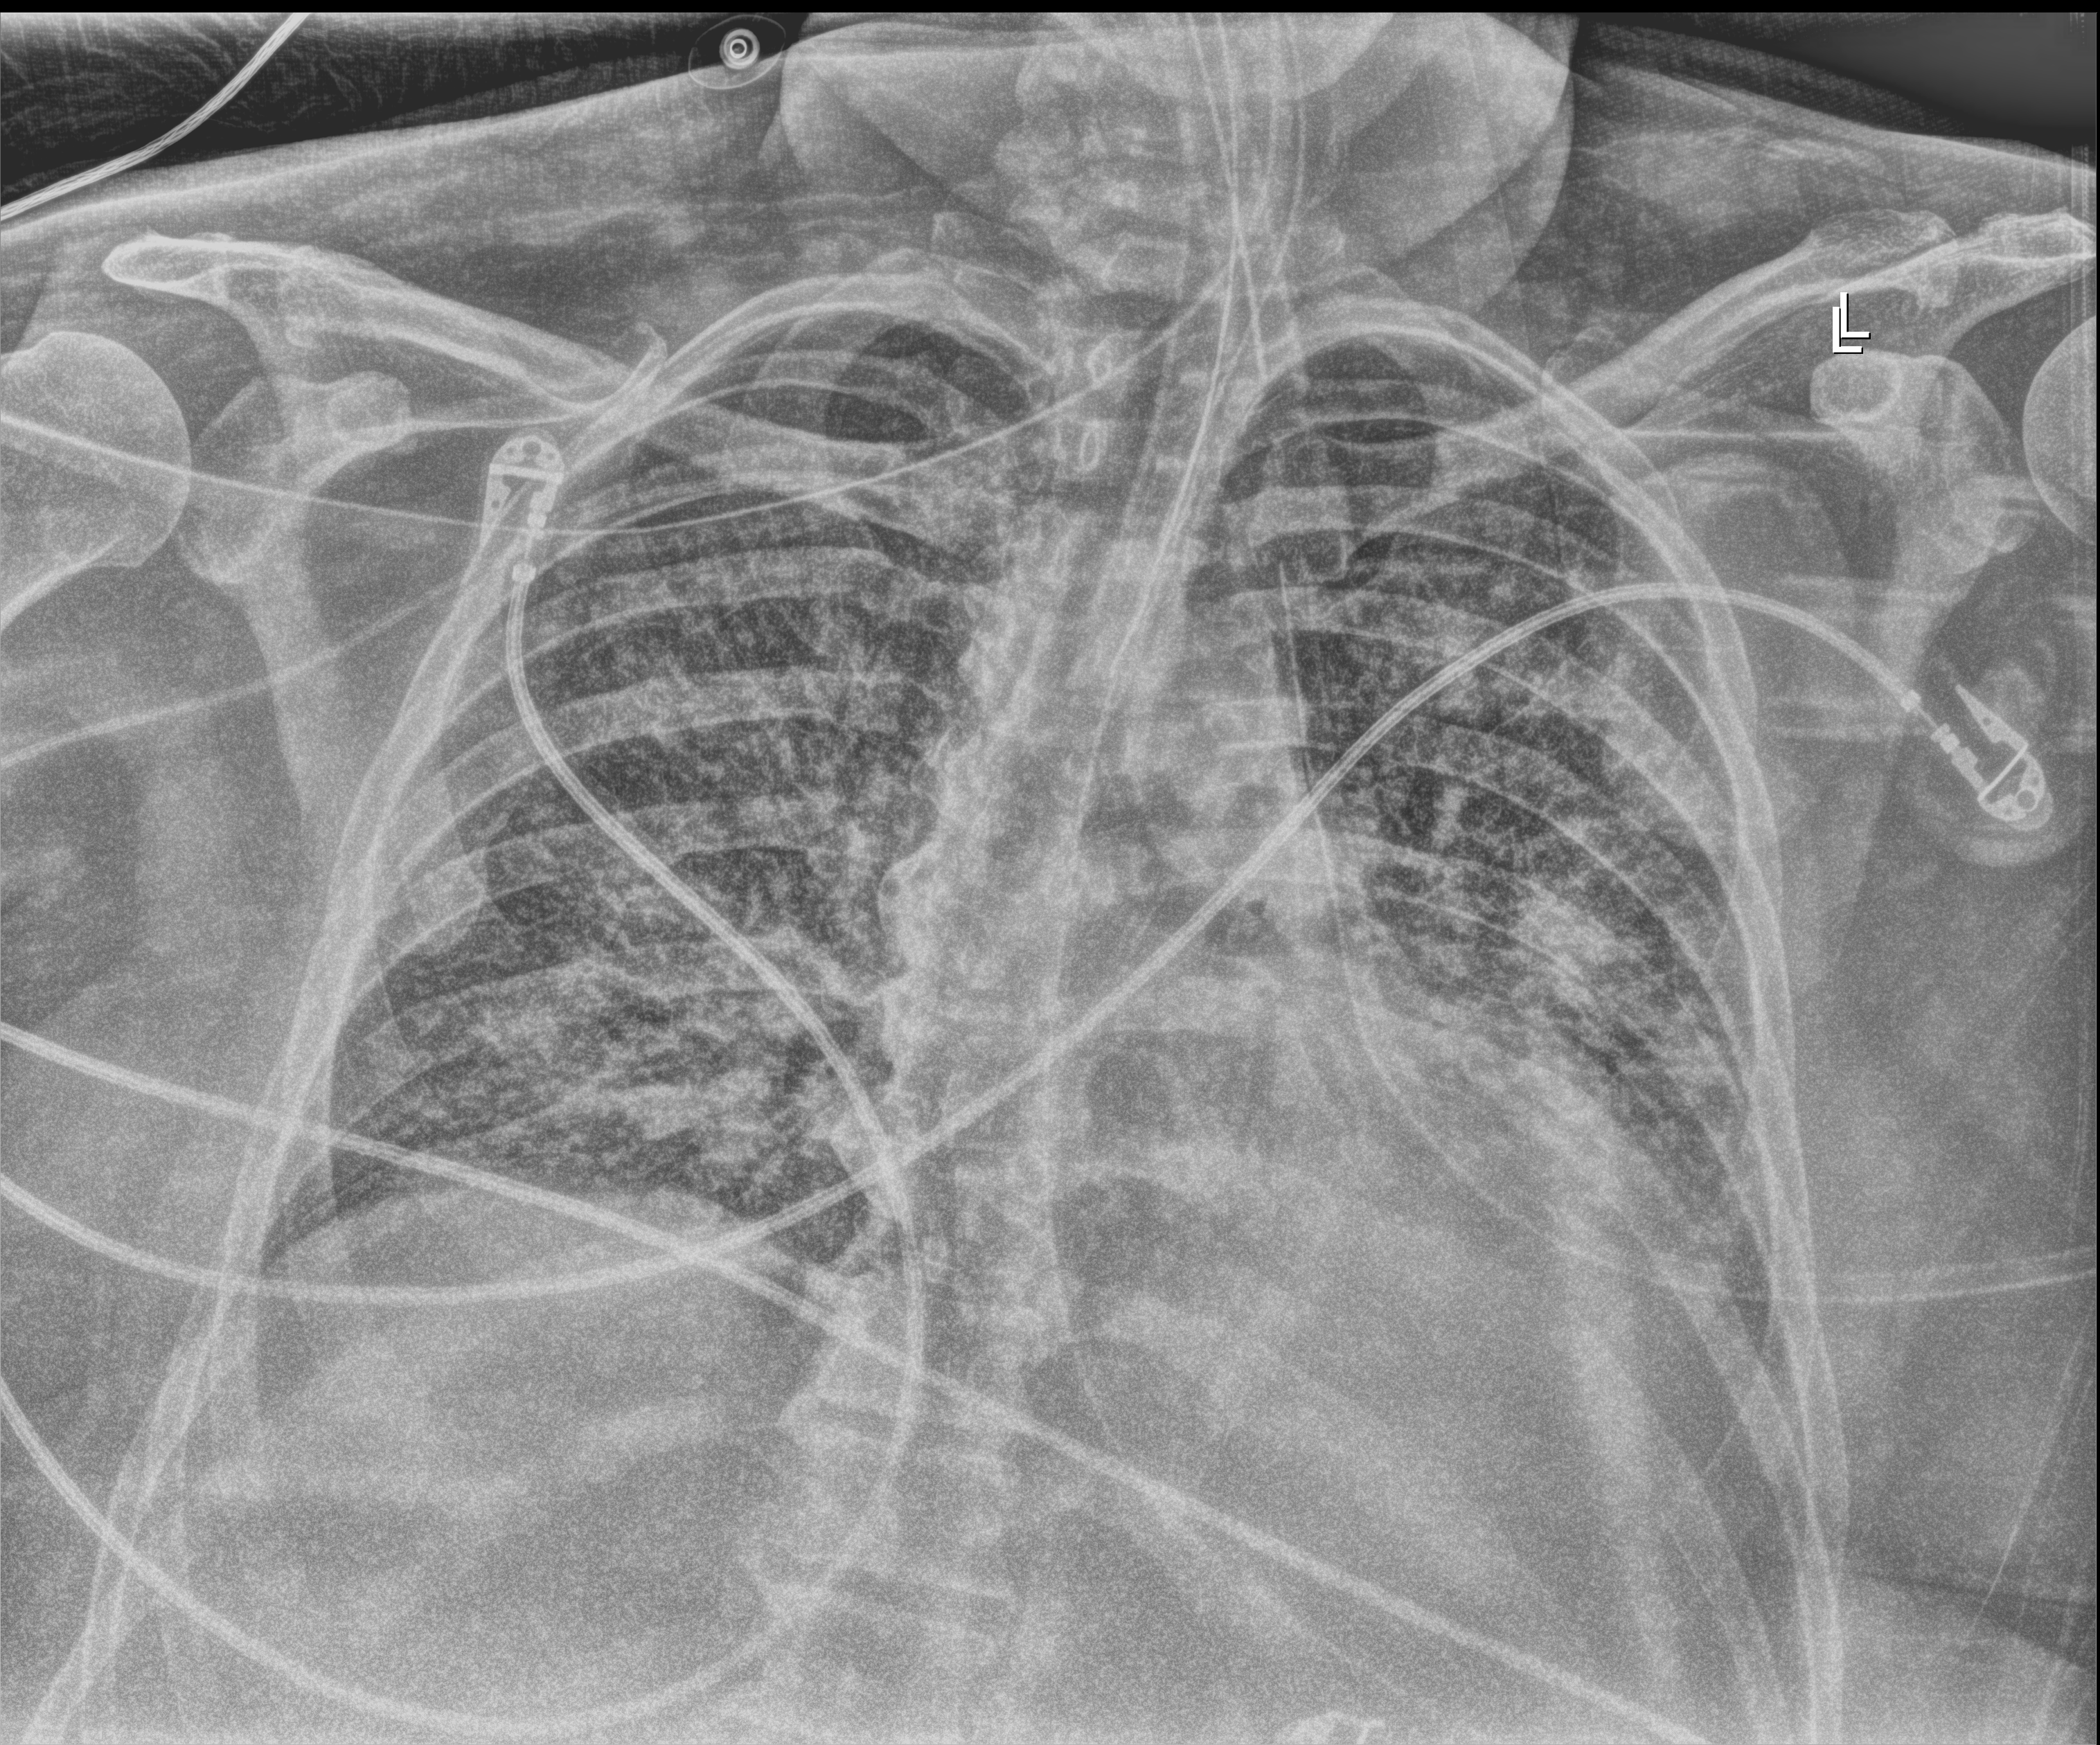
Chest X-ray, anteroposterior (AP) projection. Patient hospitalised with COVID-19, aged 18–59 years.
Hospital-stay facts (about this admission, not read from this image; timing relative to this image not recorded): admitted to intensive care during this hospital stay: yes; mechanically ventilated during this hospital stay: yes.